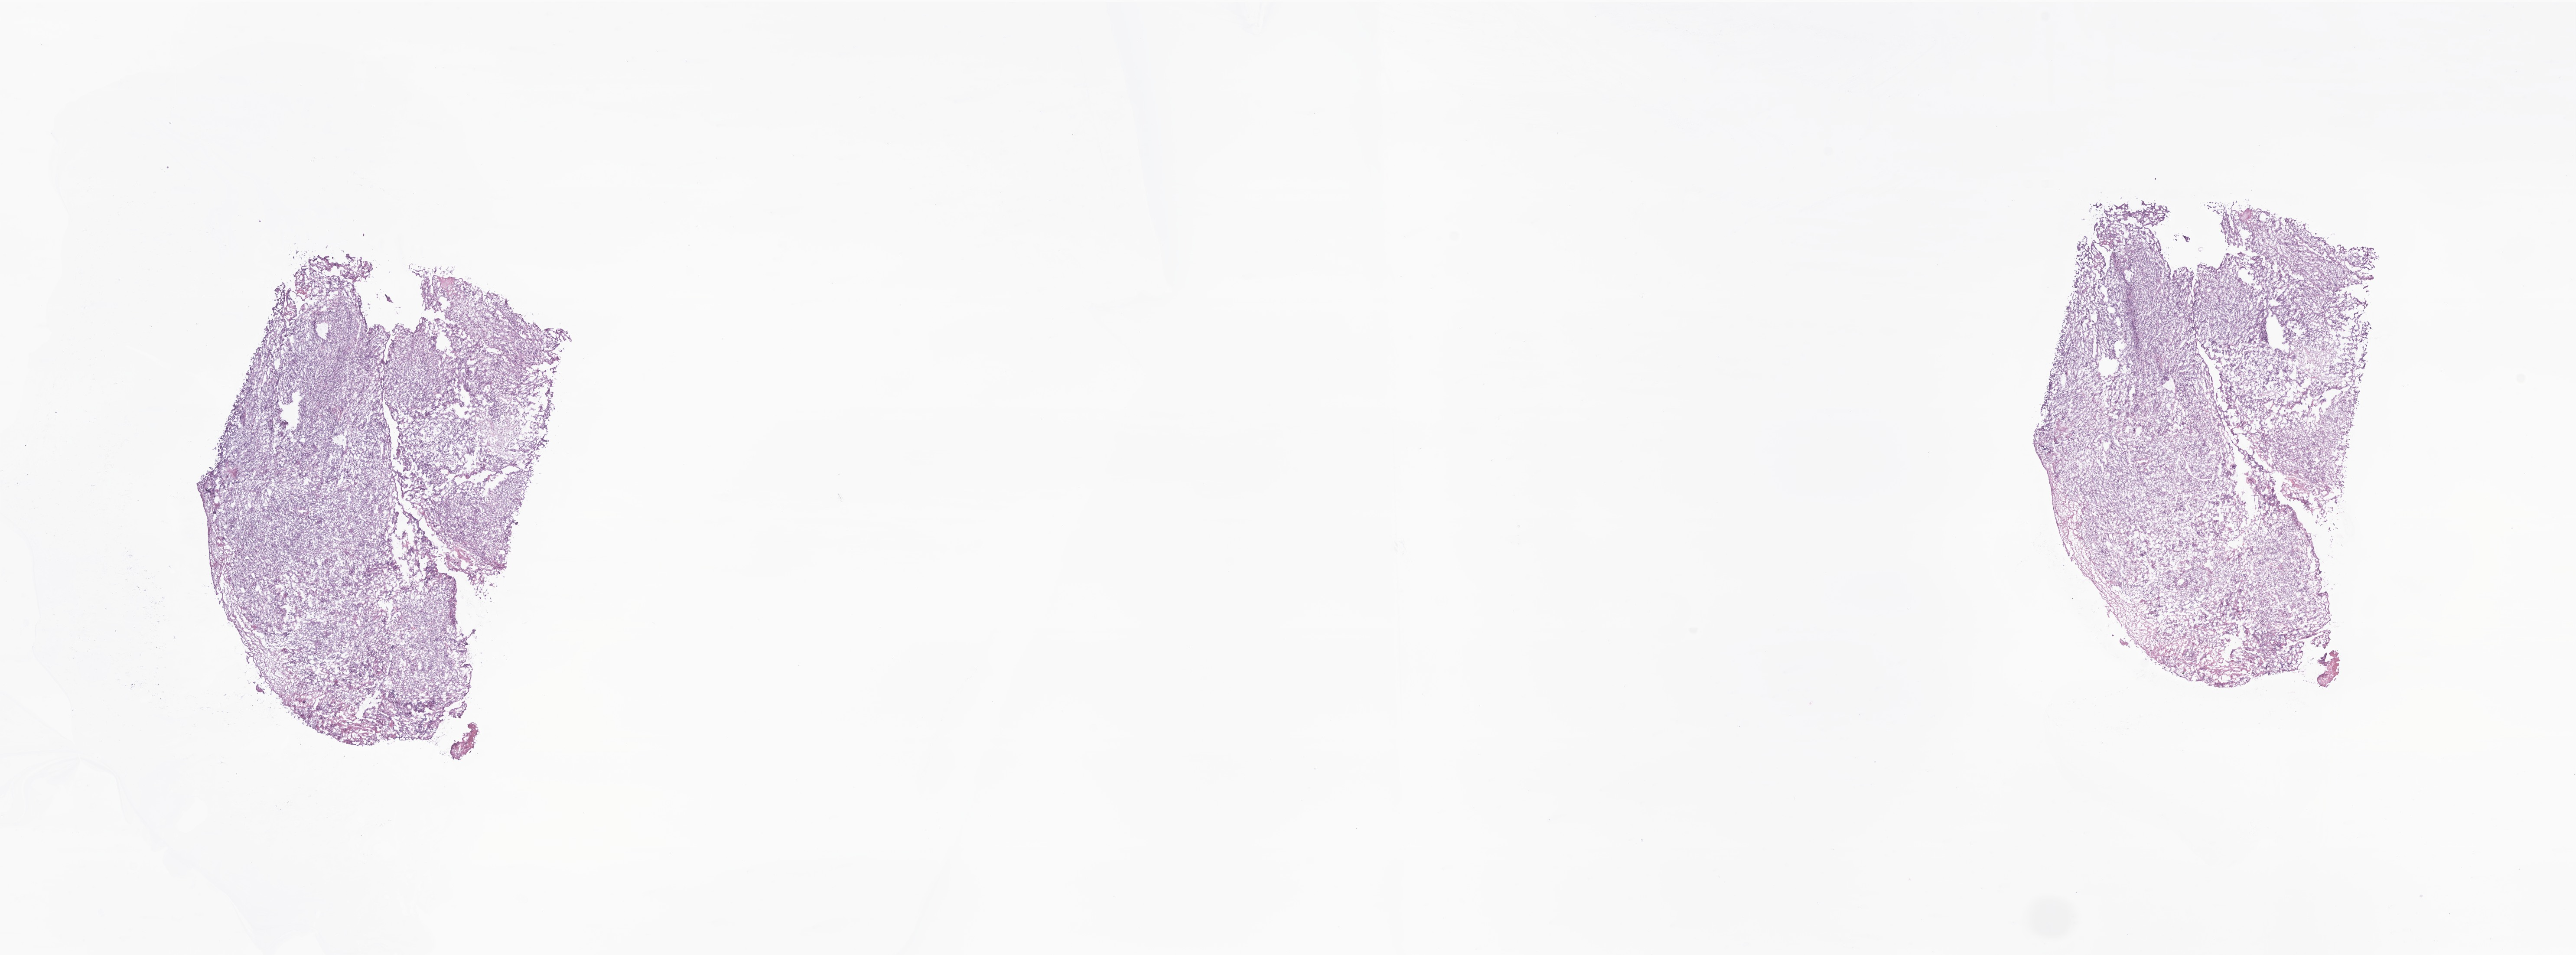
Haematoxylin and eosin whole-slide image of tumor tissue from the urinary bladder — whole scanned area (about 25.1 x 9.3 mm) shown as a low-resolution overview, frozen section (OCT-embedded). Patient female; age 49 months (4 years 1 month).
Diagnosis: Rhabdoid tumor, NOS.